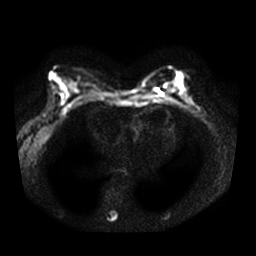
Breast MRI, one axial slice; slice 17 of 38 in the series (ordered by position); diffusion-weighted series; image 2 of 4 stored at this slice position (different b-values; order by instance number); 3 T; 5 mm slice thickness; 256 × 256 image matrix, field of view 340 × 340 mm. Female patient.
Structures marked on this image (outlined manually by an expert reader):
- tumour on diffusion-weighted imaging: bounding box [x1, y1, x2, y2] px = [175, 80, 183, 90]